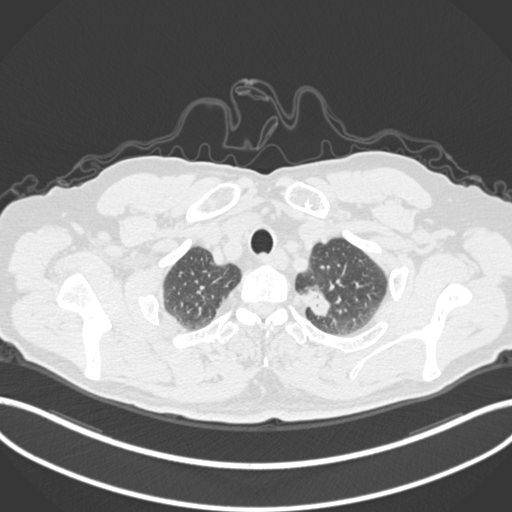
Chest CT, one axial slice. Position 285 of 306 along the scan axis. Reconstruction kernel B30f. 120 kVp. Lung window (W 1500 / L -600 HU). 1 mm slice thickness. 512 × 512 image matrix. Male patient, age 64 years. Case-level facts recorded for this patient, not image findings: clinical TNM (as recorded): T1c N0 M0.
Annotated regions visible in this slice (rectangle marked by the reading radiologist):
- lung tumour (recorded histology: adenocarcinoma): bounding box (x1, y1, x2, y2) in pixels: (297, 285, 335, 324)